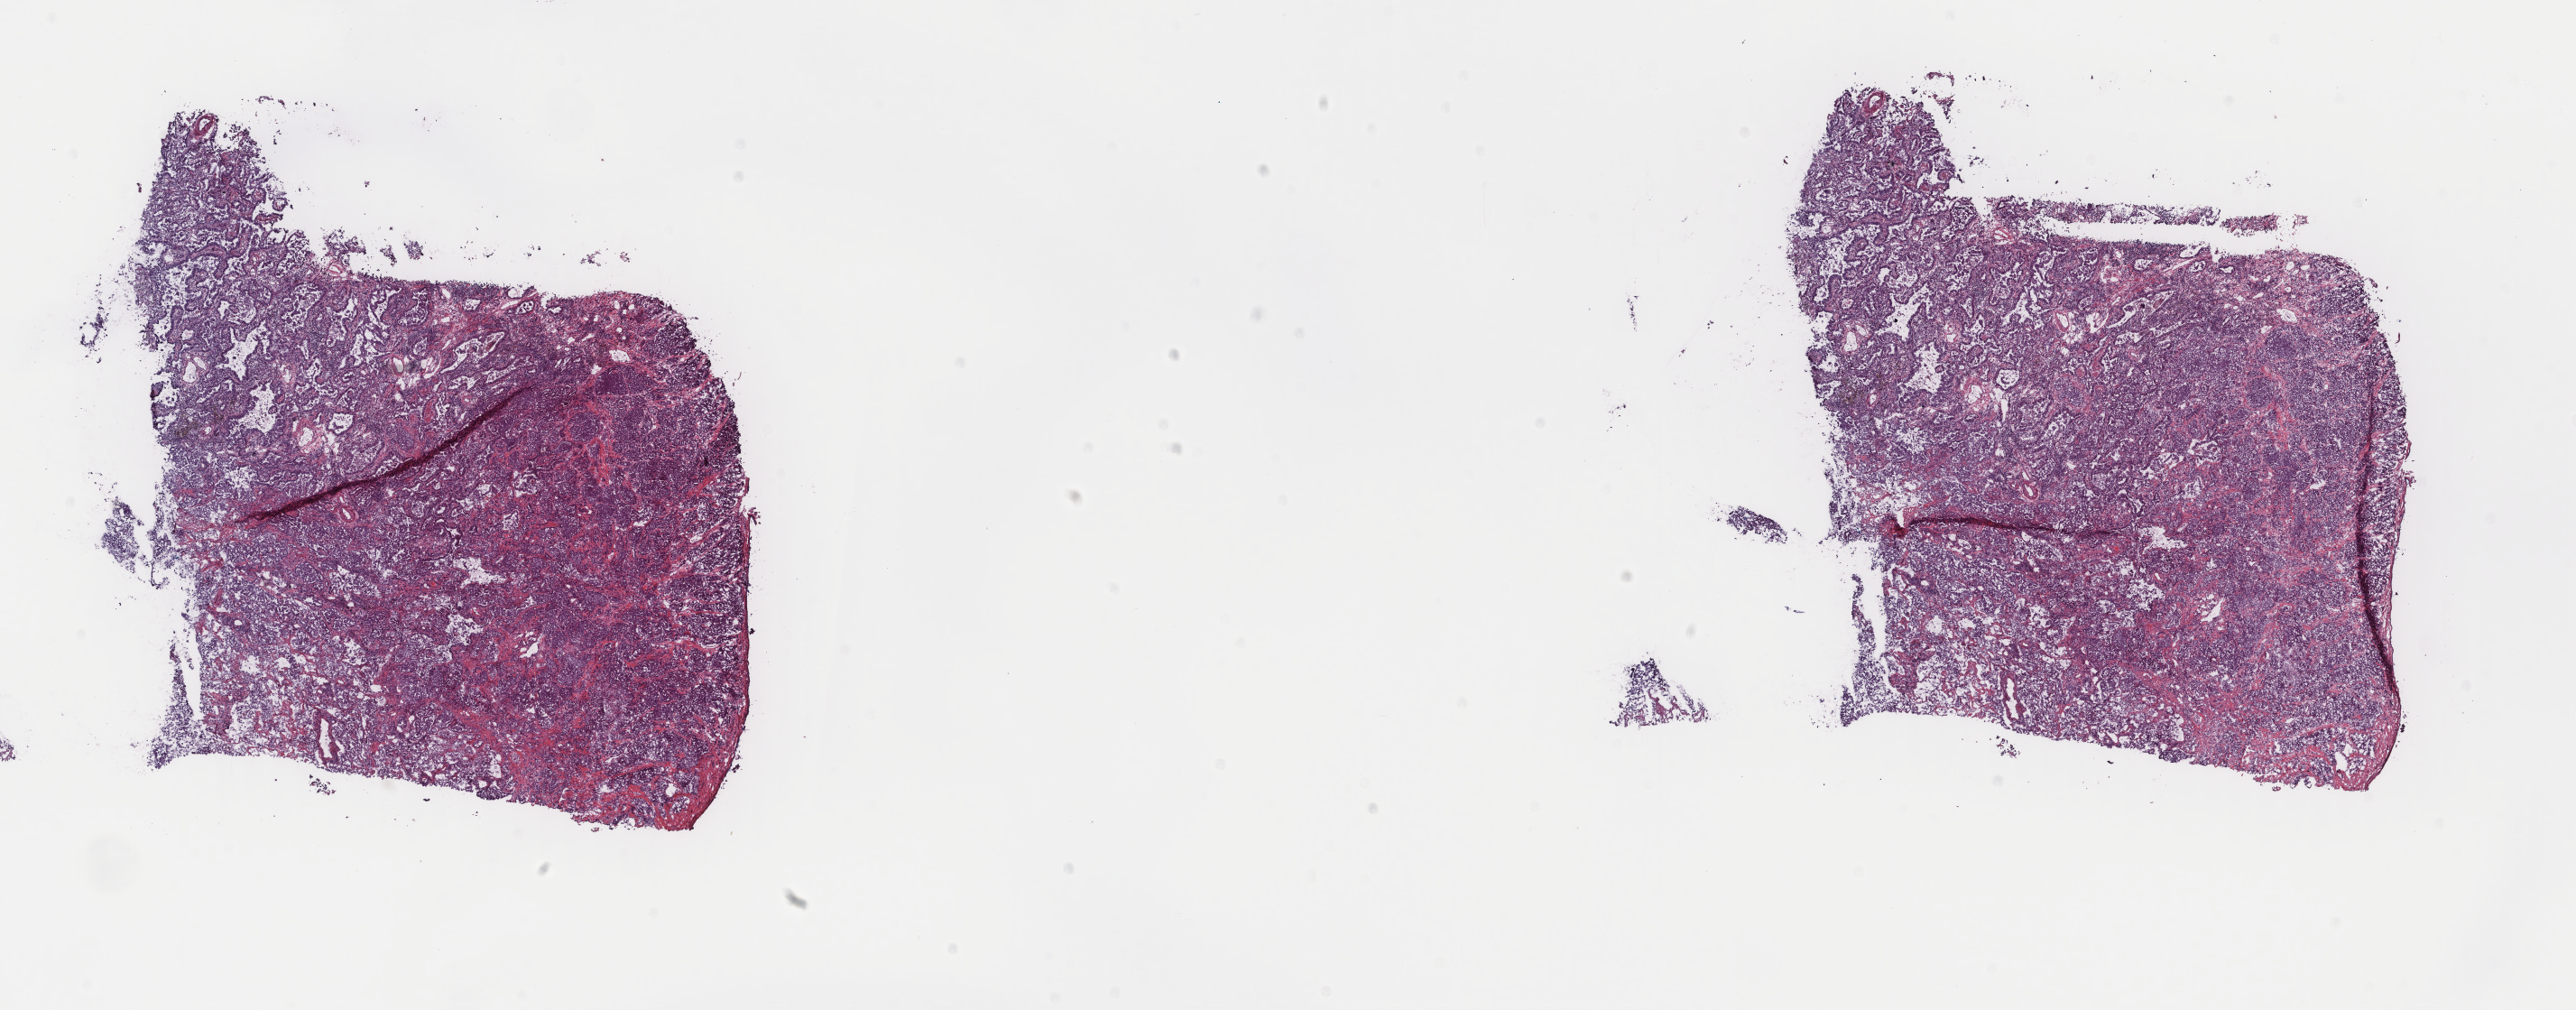
H&E-stained whole-slide image, a low-resolution overview of the entire scanned area, about 22.7 x 8.9 mm (from a 40x scan); frozen section; lung, primary tumour sample. Patient: female, age at initial diagnosis 60 years. Slide review estimates, as recorded: tumour cells 75%, tumour nuclei 75%, normal cells 0%, stromal cells 23%, necrosis 2%. Inflammatory infiltration, as recorded: lymphocyte infiltration 3%, monocyte infiltration 3%, neutrophil infiltration 5%.
Pathologic diagnosis: Adenocarcinoma, NOS (upper lobe, lung). AJCC pathologic stage: IB (6th edition).